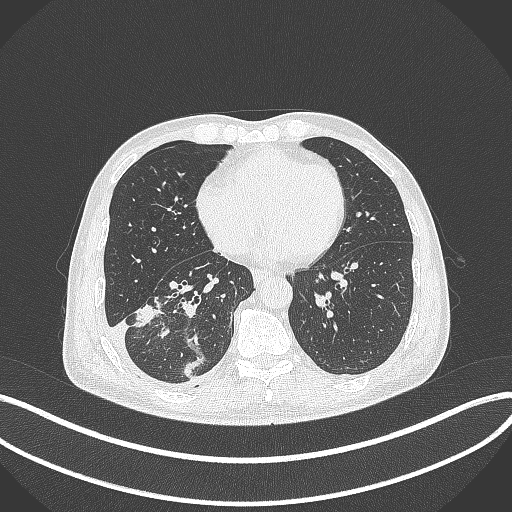
Chest CT, one axial slice. Slice 145 of 388 in the series (ordered by position). 120 kVp. Lung window (W 1500 / L -600 HU). 1 mm slice thickness. 512 × 512 image matrix, field of view 400 × 400 mm. Male patient, age 64 years. From the clinical record (not read from this slice): clinical TNM (as recorded): T3 N0 M0; histopathological grade: G2-3.
Structures marked on this image (bounding box drawn by a radiologist):
- lung tumour (recorded histology: adenocarcinoma): box from (x=134, y=302) to (x=167, y=329) px